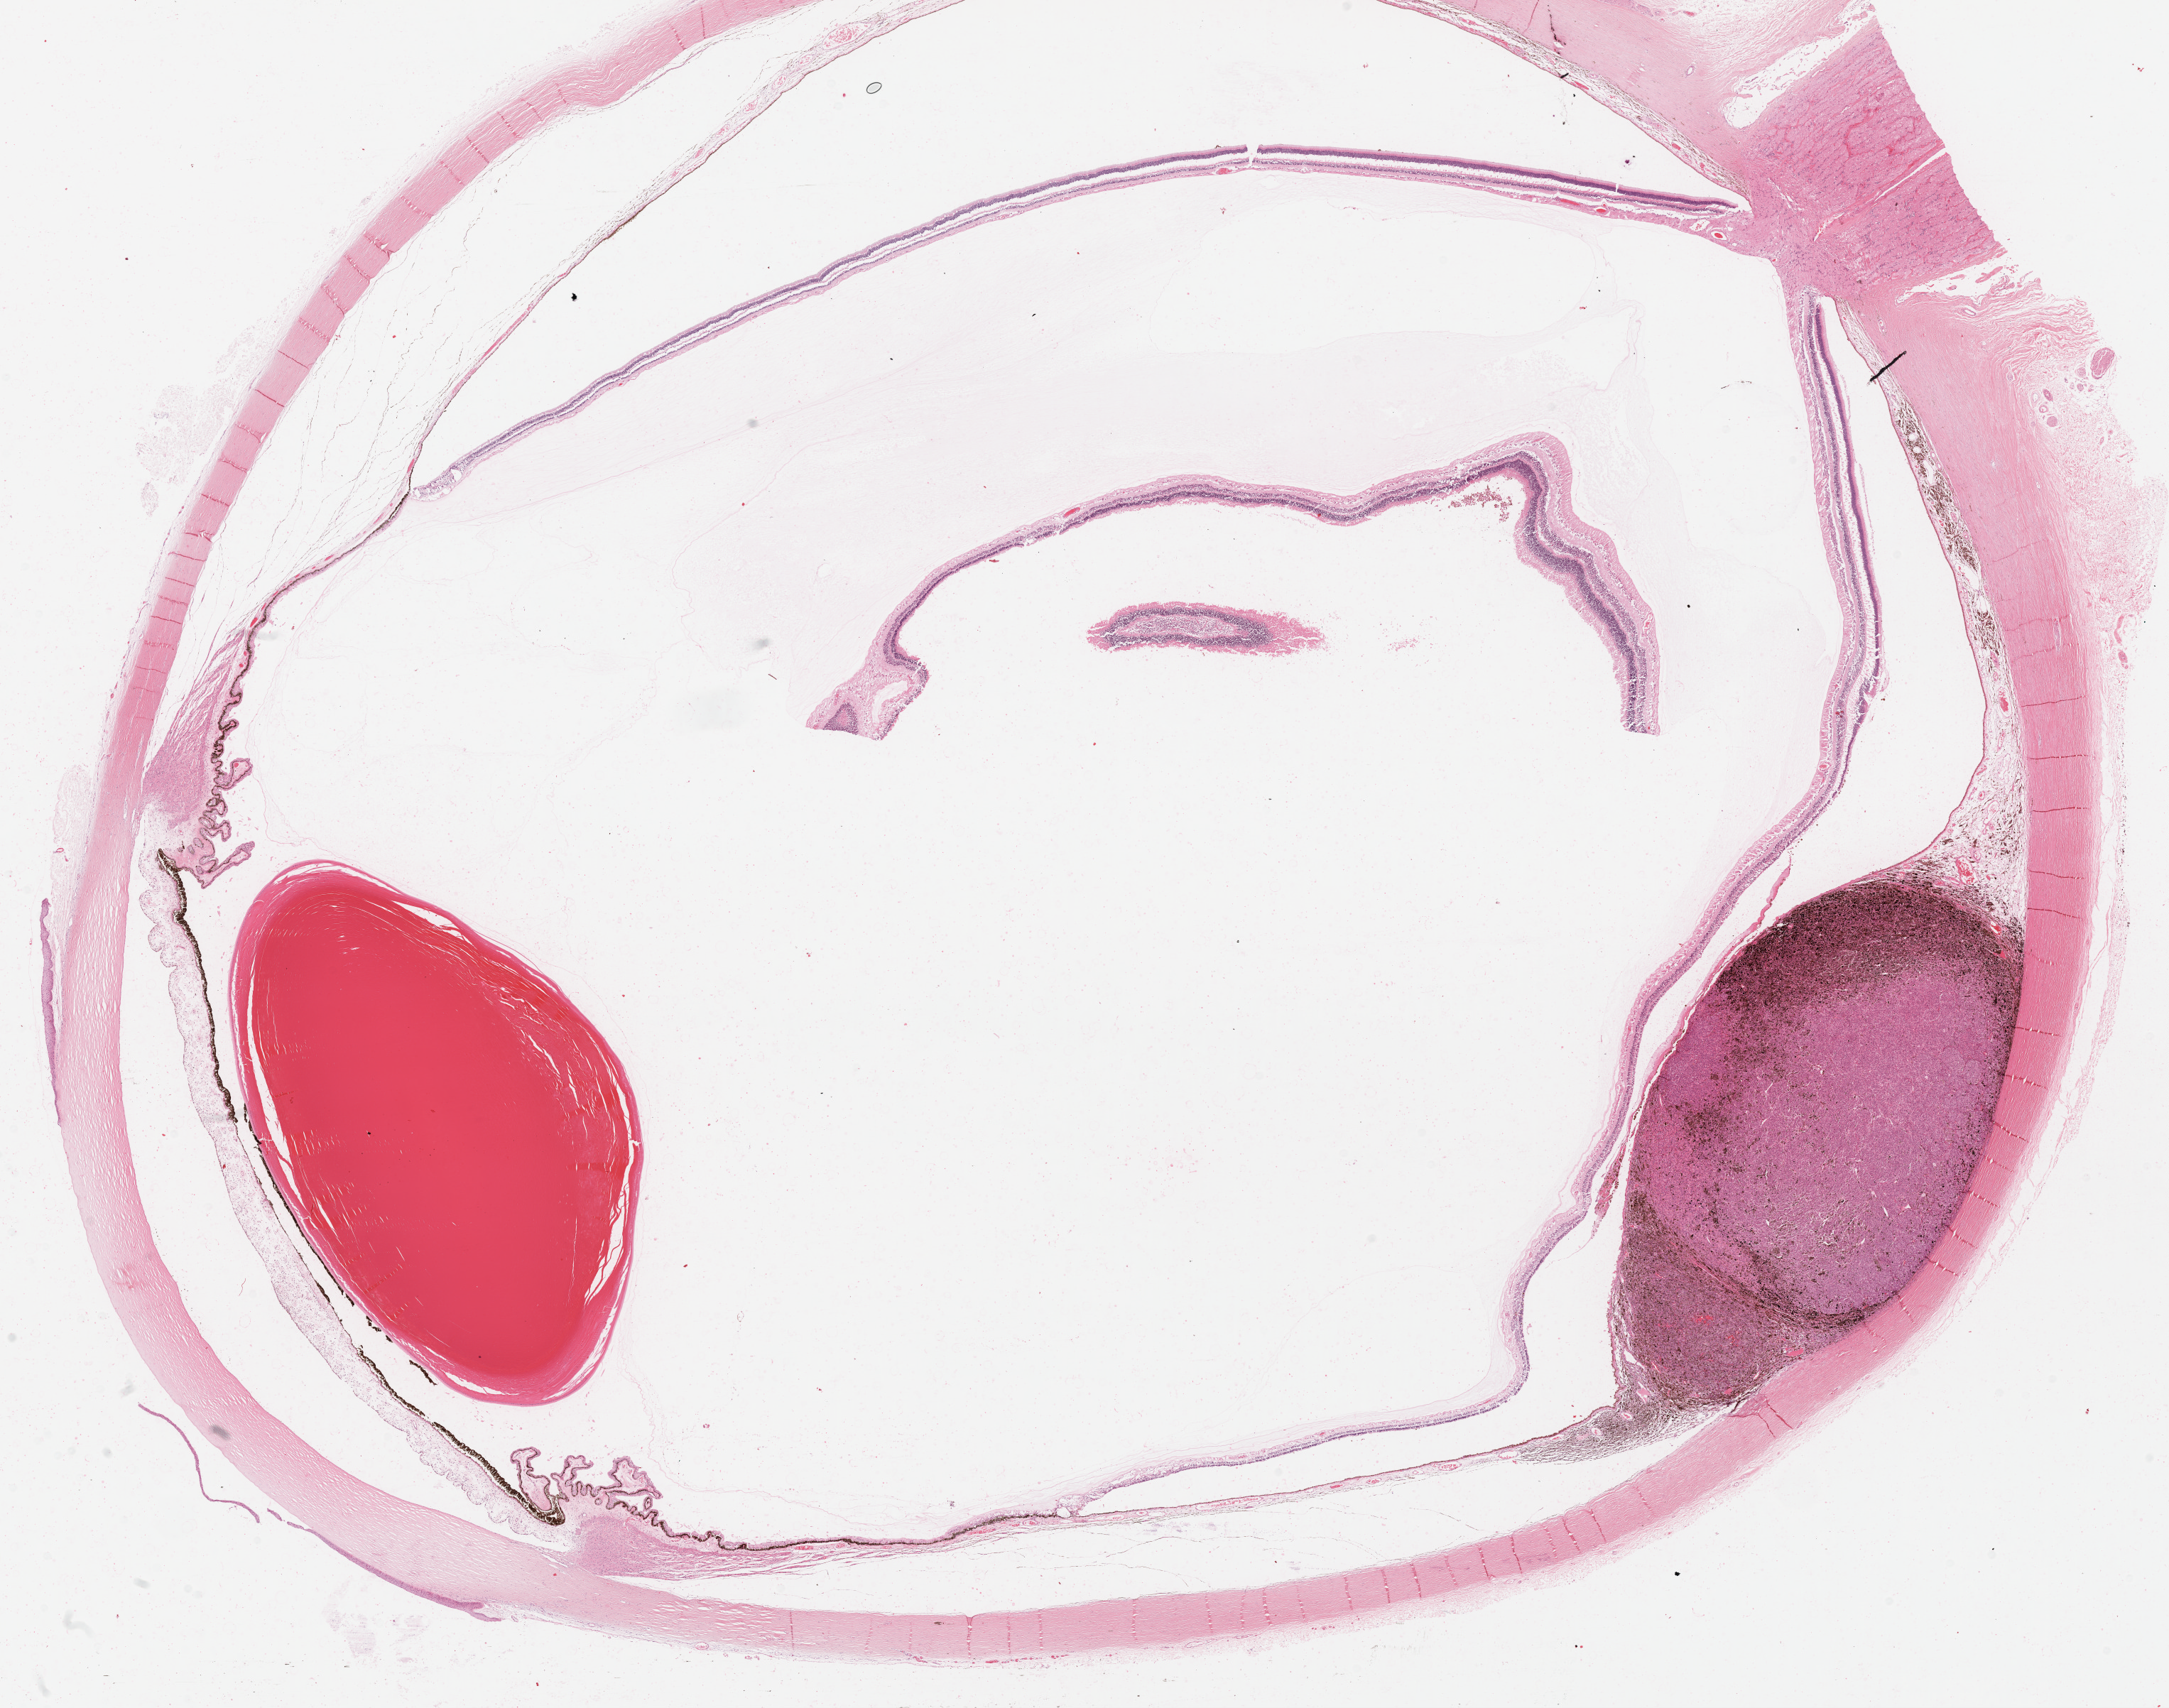
H&E whole-slide image, shown as a low-resolution overview of the whole scanned area (about 24.6 x 19.4 mm, from a 20x scan). Formalin-fixed paraffin-embedded (FFPE) diagnostic section. Primary tumour sample from the uvea. Female patient; age at initial diagnosis 60 years. Slide review estimates, as recorded: tumour cells 50%, tumour nuclei 60%, normal cells 50%, stromal cells 0%, necrosis 0%. Infiltration values recorded for this section: lymphocyte infiltration 1%, monocyte infiltration 0%, neutrophil infiltration 0%.
Laterality: left. AJCC pathologic stage: IIA (7th edition). Diagnosis: Mixed epithelioid and spindle cell melanoma (choroid).